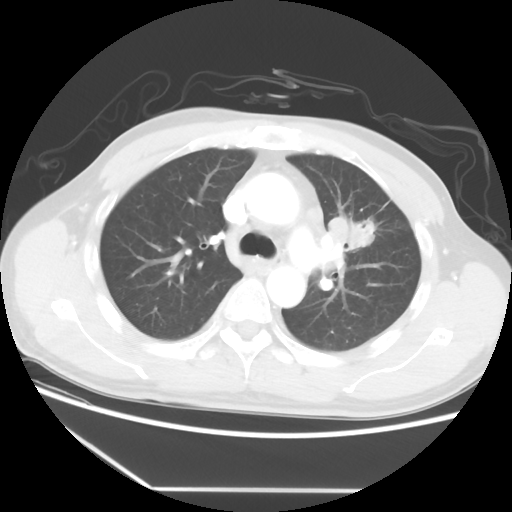
Chest CT, one axial slice. Slice 37 of 56 in the series (ordered by position). 120 kVp. Lung window (W 1500 / L -600 HU). 5 mm slice thickness. 512 × 512 image matrix. Male patient, age 53 years. Case-level facts recorded for this patient, not image findings: clinical TNM (as recorded): T2a N1 M1b.
Structures marked on this image (rectangle marked by the reading radiologist):
- lung tumour (recorded histology: adenocarcinoma): box from (x=330, y=215) to (x=375, y=249) px